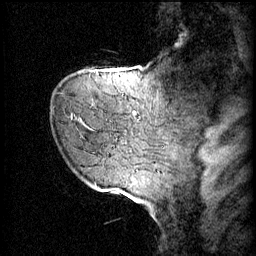
Breast MRI (dynamic contrast-enhanced), one sagittal slice. Position 11 of 60 along the scan axis. 4 images stored at this slice position (order not interpretable as contrast timing). 1.5 T. TE 4.2 ms, TR 11 ms. 2 mm slice thickness. 256 × 256 image matrix, field of view 220 × 220 mm. Female patient, age 72 years.
Structures marked on this image (semi-automatically segmented with operator editing):
- analysis volume of interest (the breast-tissue region the enhancement analysis was run in; not a lesion): bounding box <79,70,109,121> (left, top, right, bottom; pixels)
- tumour enhancement mask (voxels above the 70 % enhancement threshold inside the analysis volume of interest): <88,72,97,75>